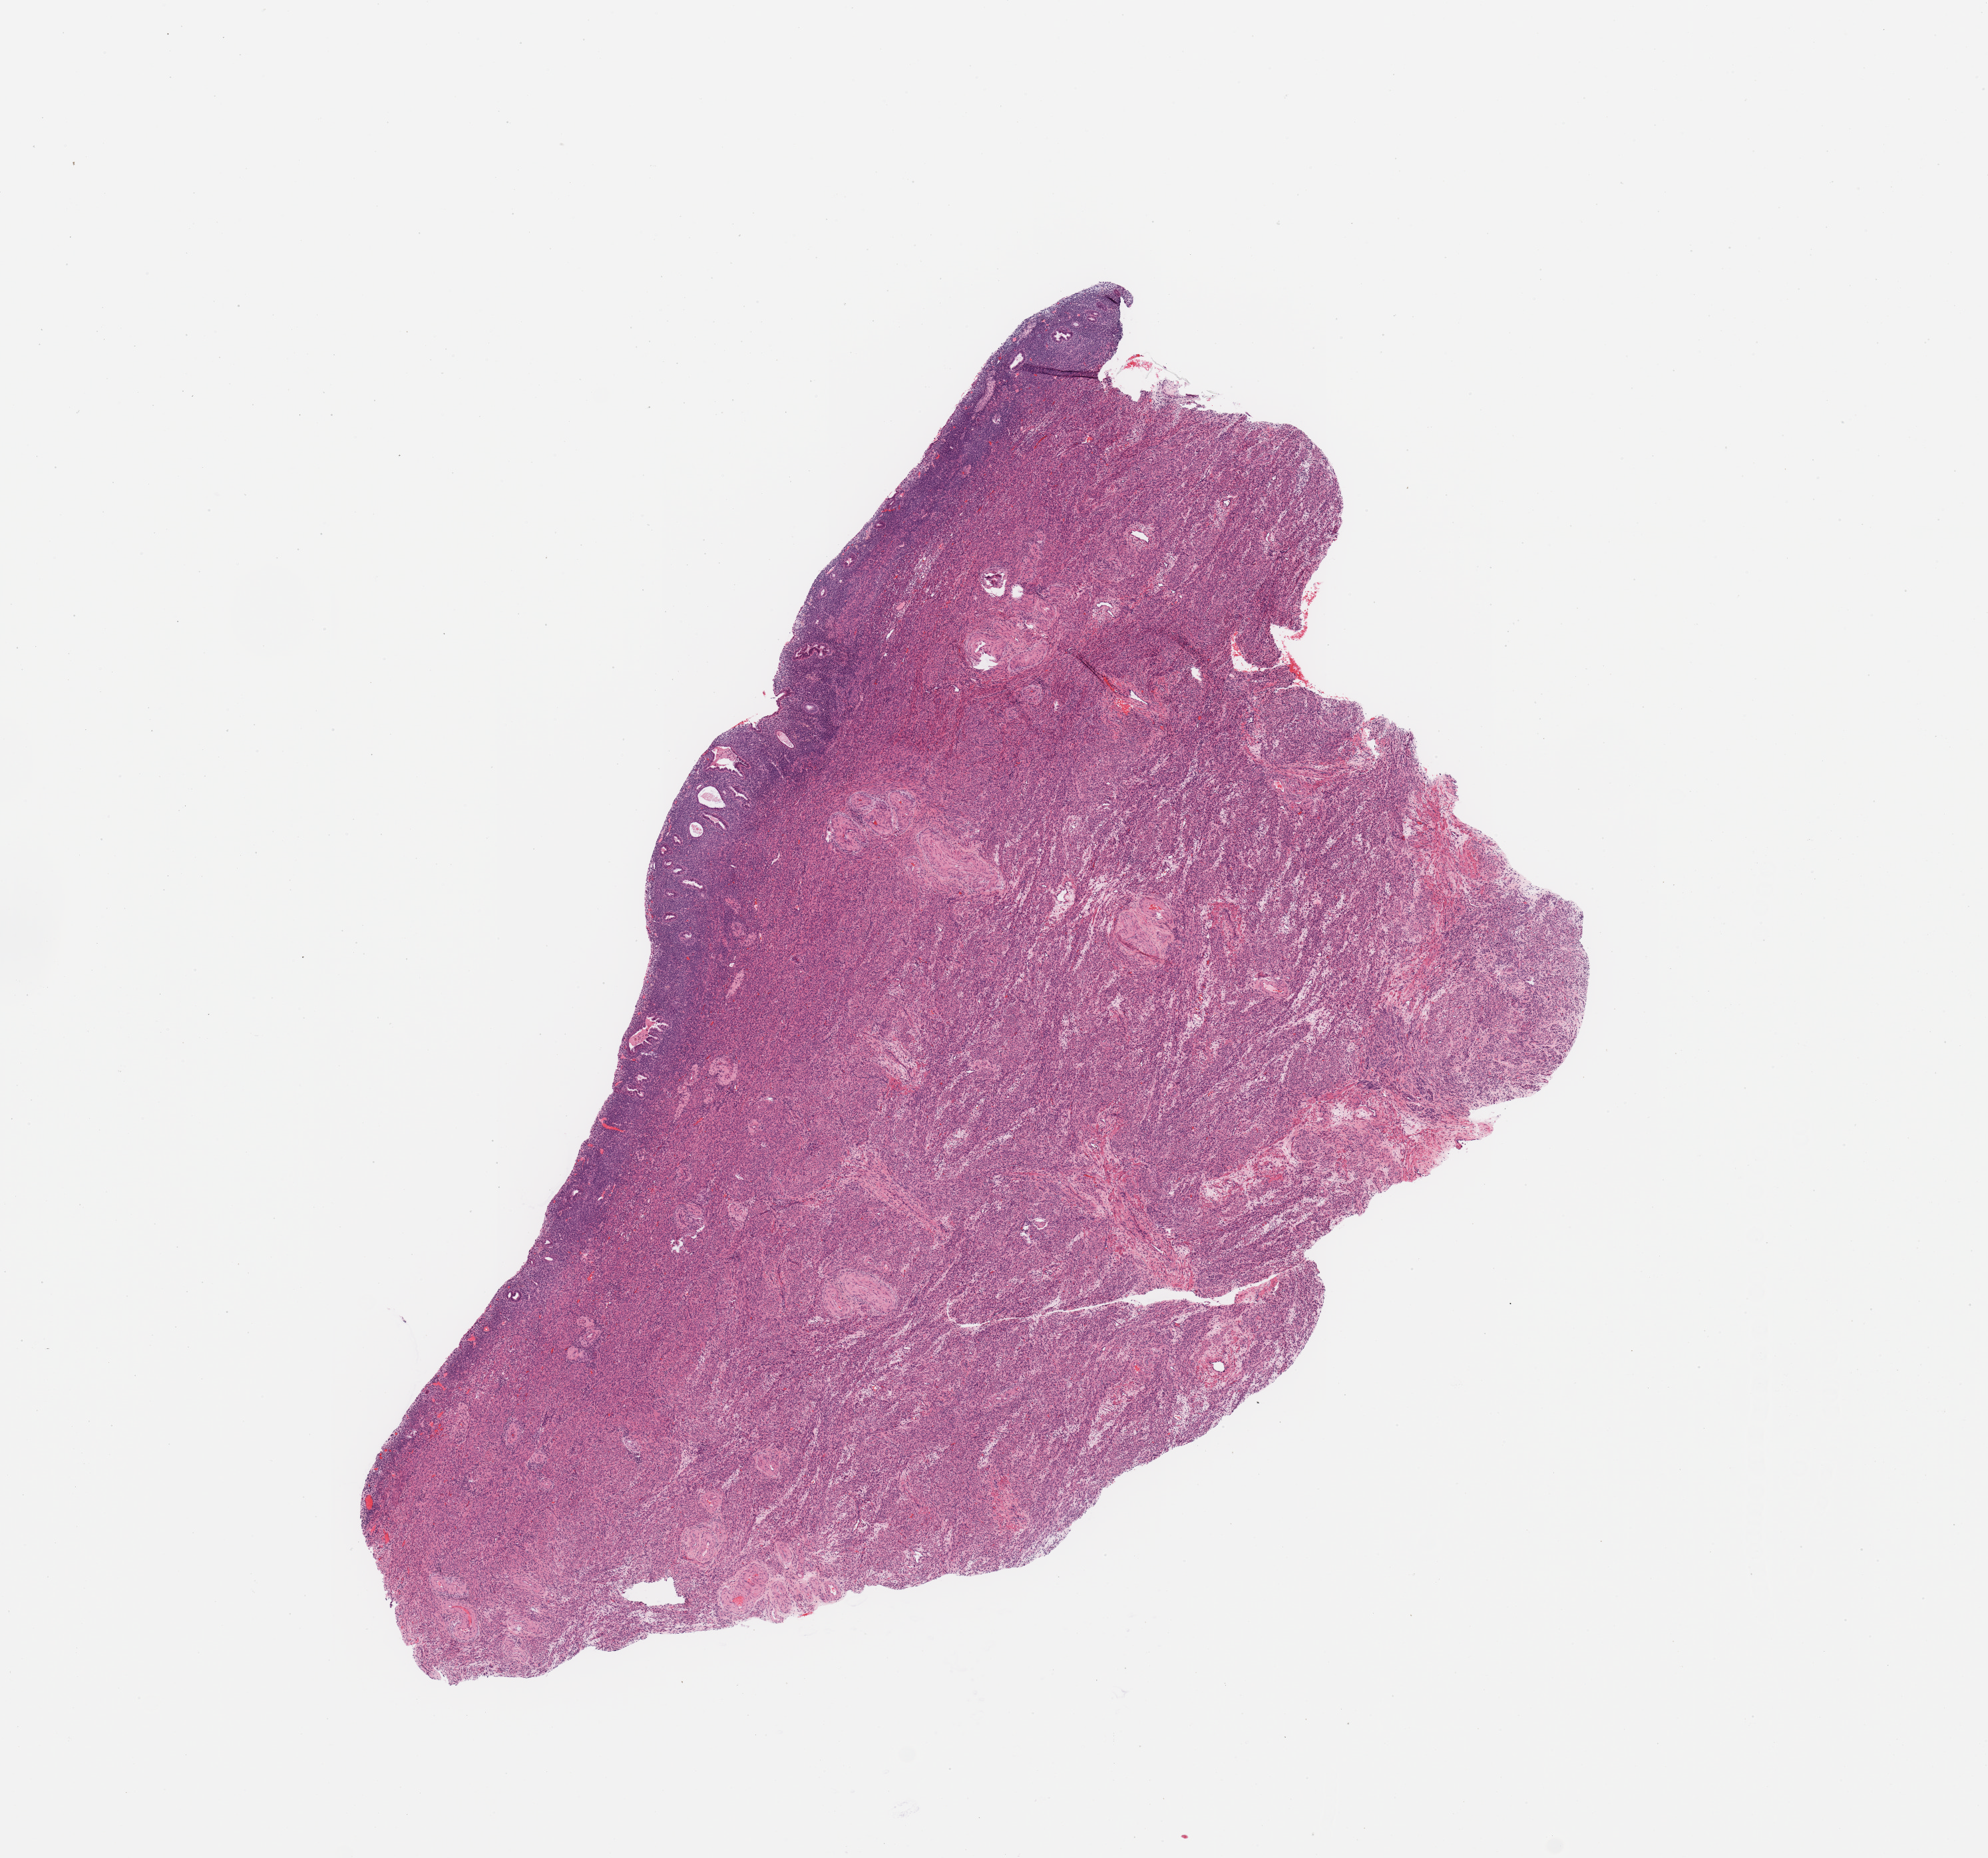
Digitized H&E-stained tissue section (whole slide), shown as a low-resolution overview of the whole scanned area (about 11.8 x 11.0 mm), normal (non-tumour) tissue sample, sampled site: uterus. Female, 60 y/o.
This section: normal (non-tumour) tissue from the same patient. Patient diagnosis: Endometrioid adenocarcinoma, NOS.